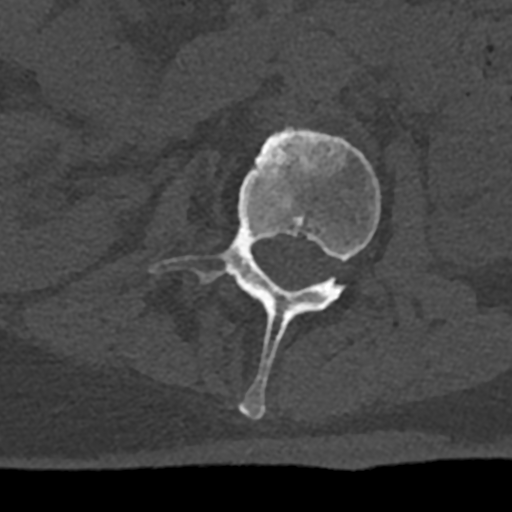
CT including the spine, one axial slice. Position 374 of 797 along the scan axis. Reconstruction kernel Br40s/3. 120 kVp. Bone window (W 1800 / L 400 HU). 0.5 mm slice thickness. 512 × 512 image matrix, field of view 160 × 160 mm. Patient: male, 74 years. Case-level facts recorded for this patient, not image findings: primary cancer: renal; vertebrae with lytic lesions (as recorded): T10, L1, L2, L3, L4, L5.
Structures marked on this image (semi-automatic segmentation, software-assisted and operator-edited):
- L2 vertebra: box from (x=149, y=127) to (x=381, y=420) px